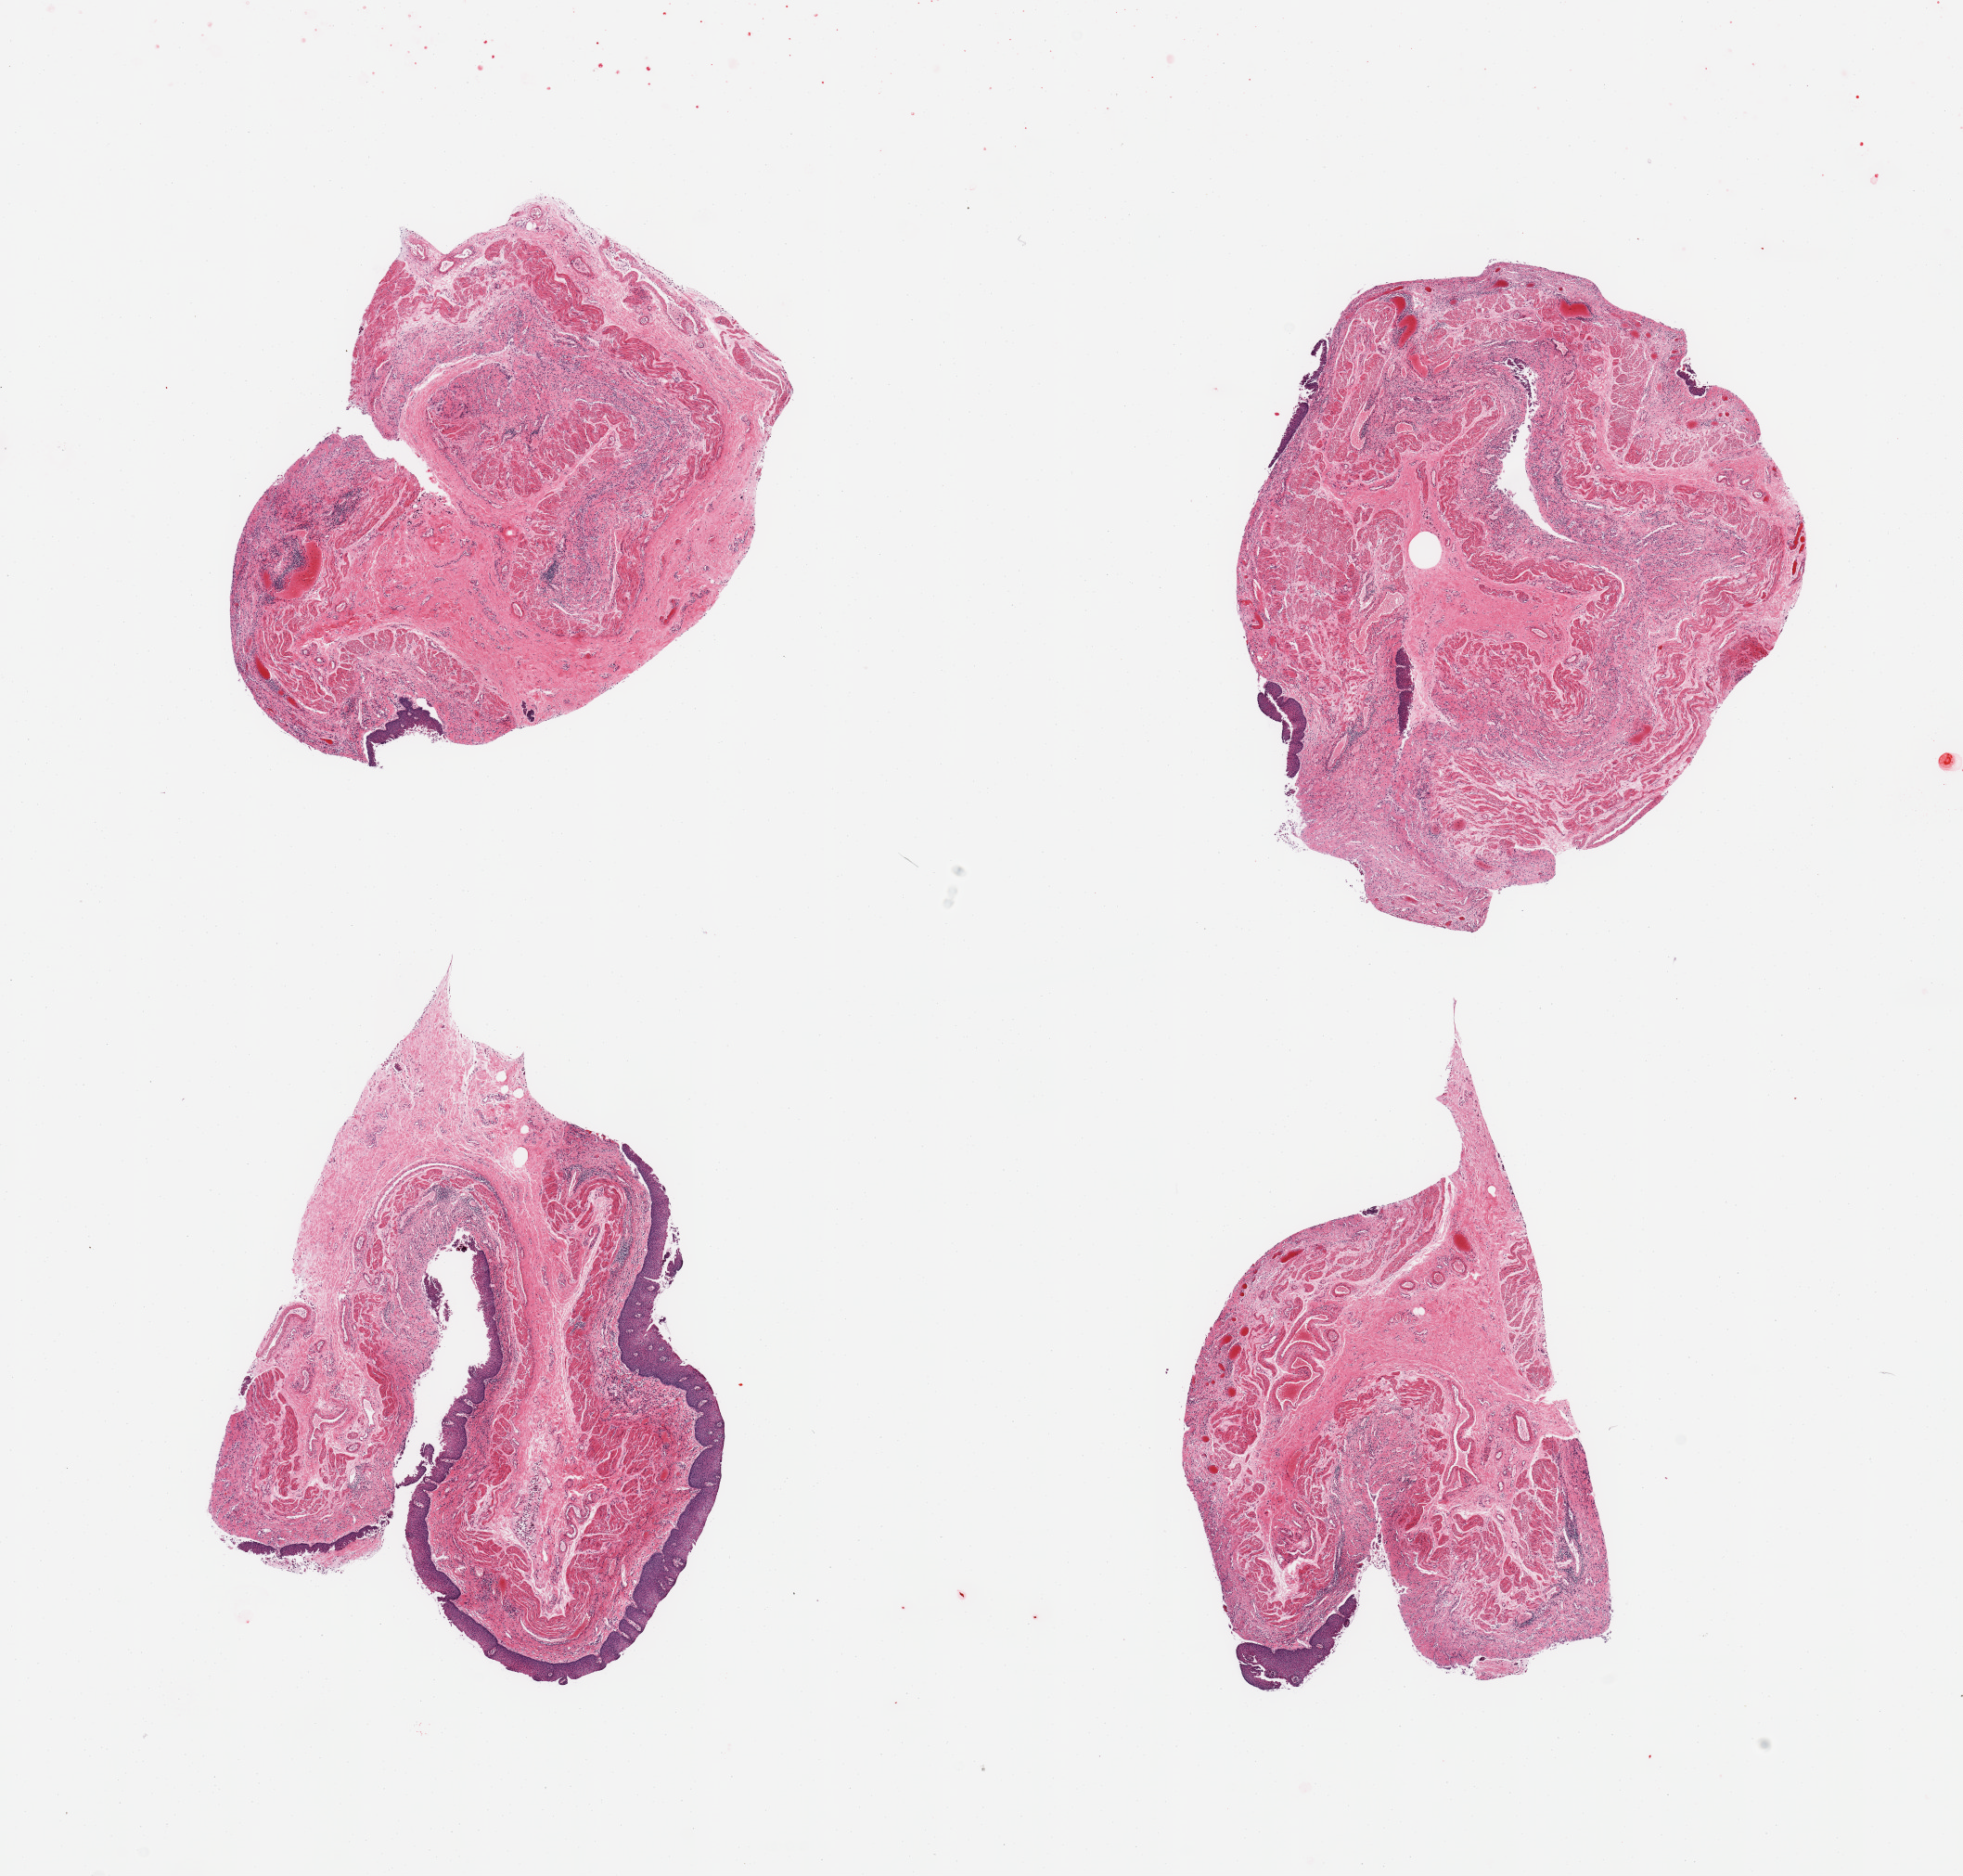
Digitized hematoxylin and eosin (H&E)-stained section — whole scanned area (about 16.7 x 16.0 mm) shown as a low-resolution overview. PAXgene-fixed, paraffin-embedded tissue. Section of esophageal mucous membrane (target tissue). Tissue donor sample. Donor sex: female.
Pathologist's review note for this sample: 4 pieces, target squamous mucosa up to ~0.25mm, sloughing.